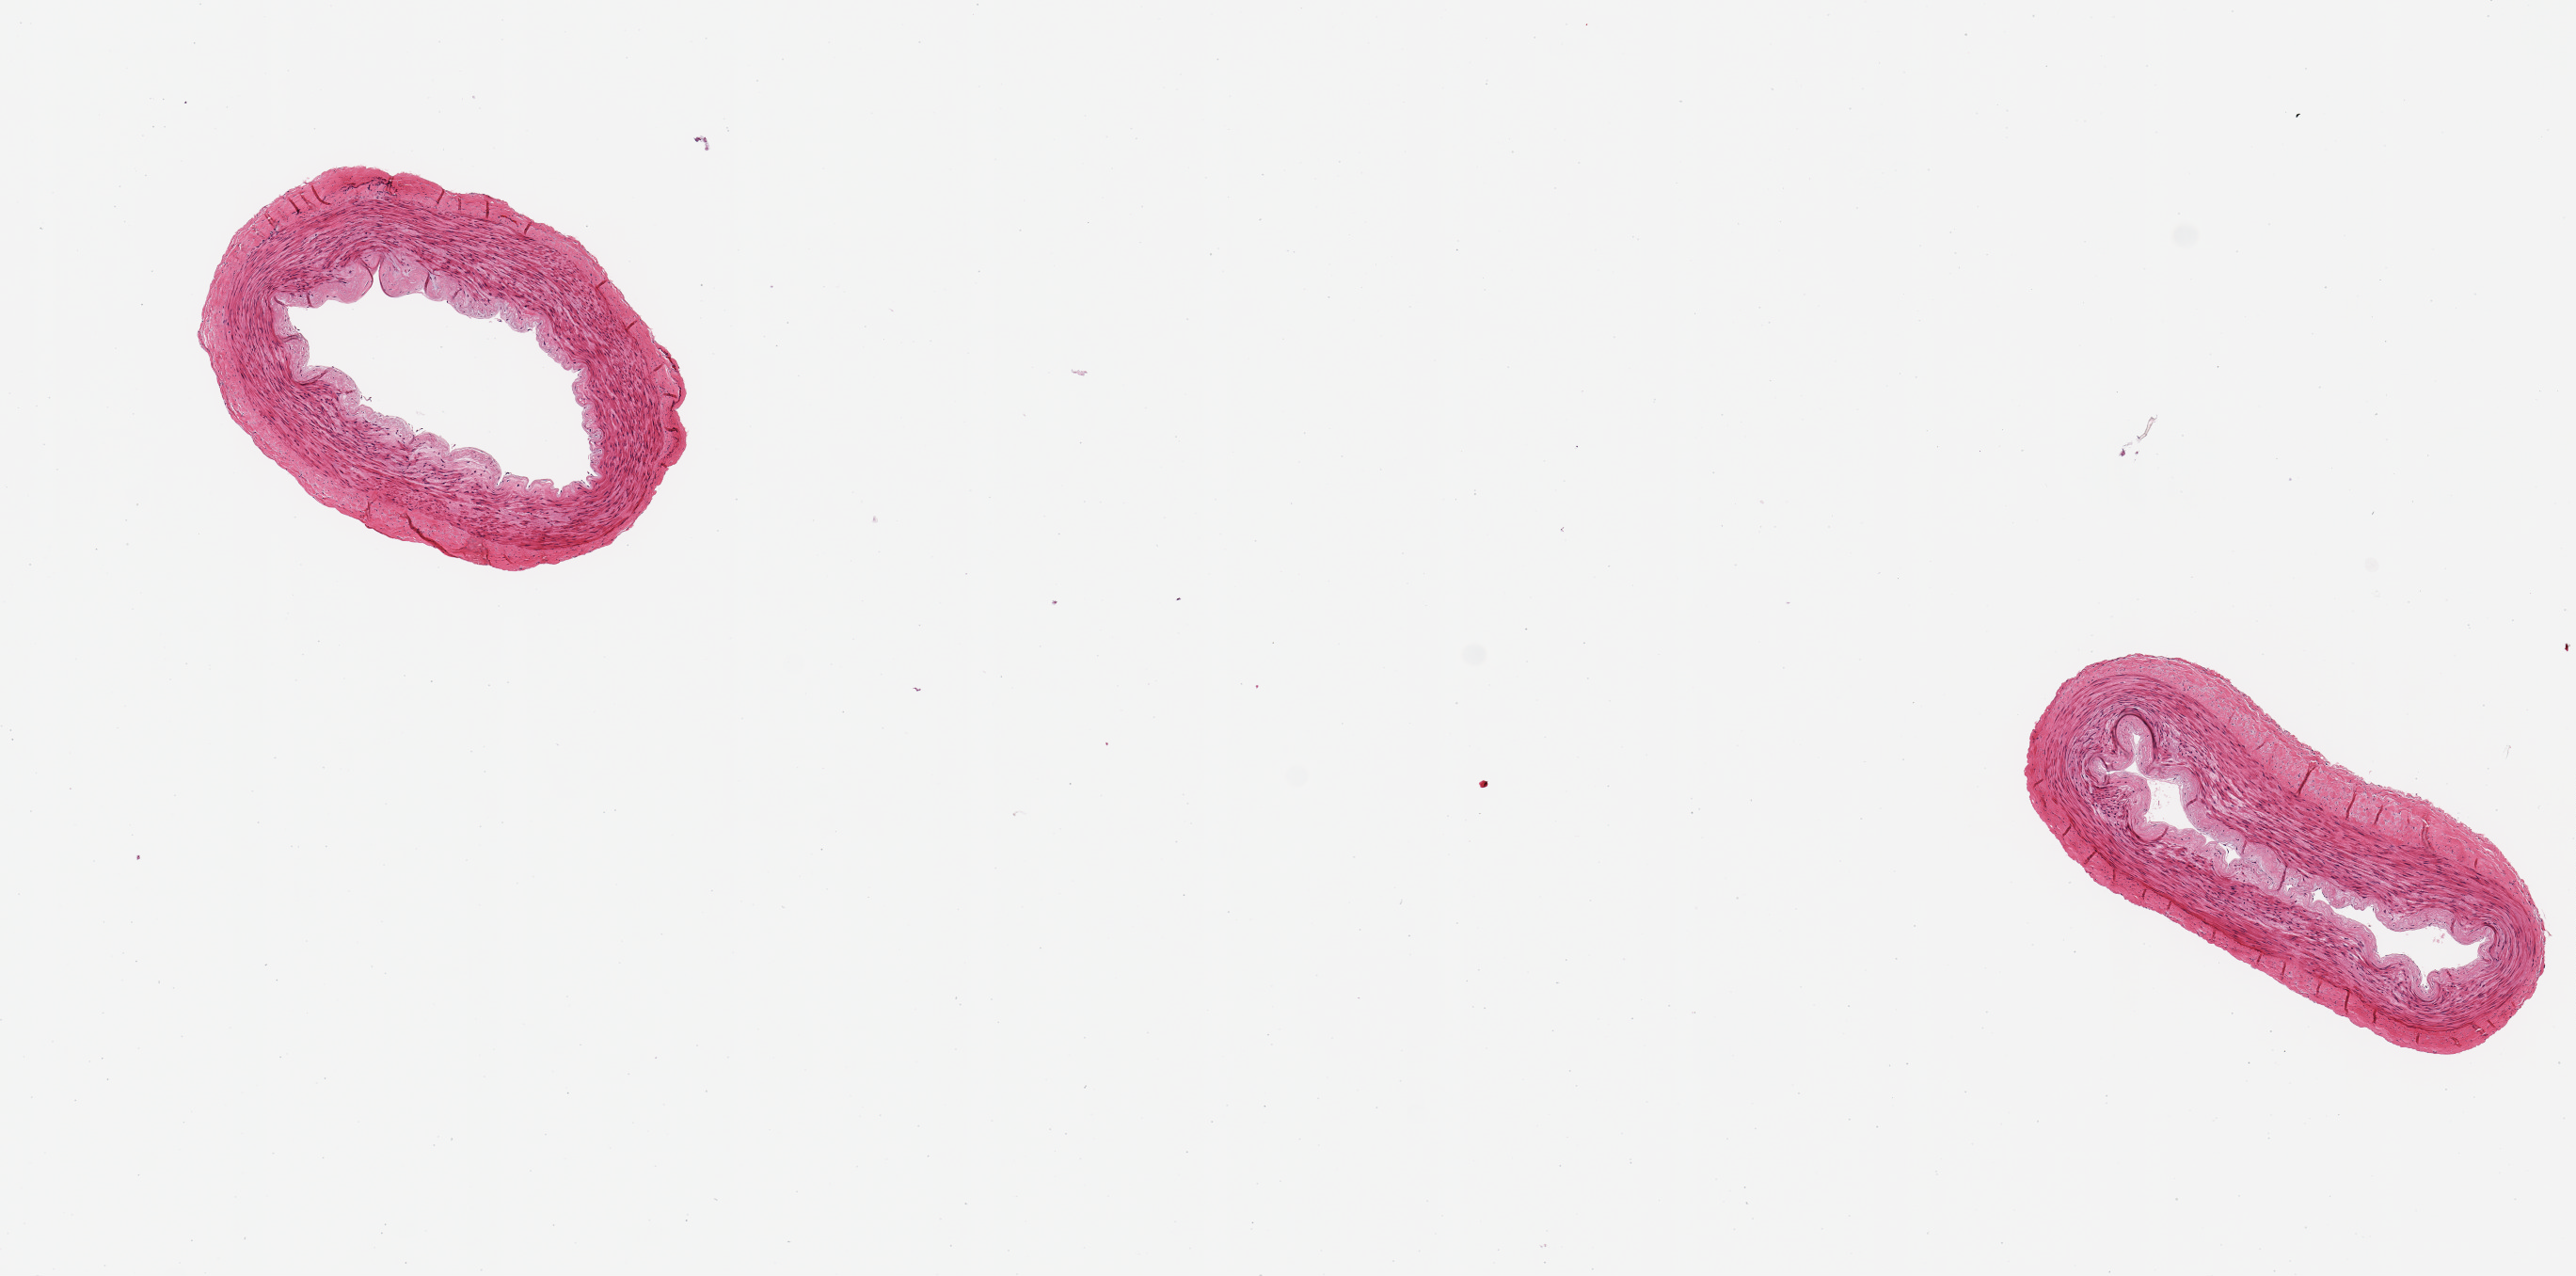
Hematoxylin and eosin (H&E) whole-slide image, brightfield — whole scanned area (about 10.8 x 5.4 mm) shown as a low-resolution overview, PAXgene-fixed paraffin-embedded (PFPE) section, target tissue: tibial artery, tissue donor sample. Donor sex: female.
• reviewer comment on this tissue sample: 2 pieces; no lesions; well trimmed